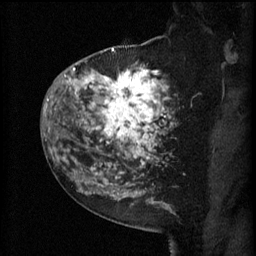
Breast MRI (dynamic contrast-enhanced), one sagittal slice. Slice 41 of 60 in the series (ordered by position). 3 images stored at this slice position (order not interpretable as contrast timing). 1.5 T. TE 4.2 ms, TR 11 ms. 2 mm slice thickness. 256 × 256 image matrix, field of view 180 × 180 mm. Patient: female, 52 years.
Structures marked on this image (semi-automatic segmentation, software-assisted and operator-edited):
- analysis volume of interest (the breast-tissue region the enhancement analysis was run in; not a lesion): box from (x=81, y=52) to (x=174, y=157) px
- tumour enhancement mask (voxels above the 70 % enhancement threshold inside the analysis volume of interest): (x=81, y=68)–(x=173, y=157)